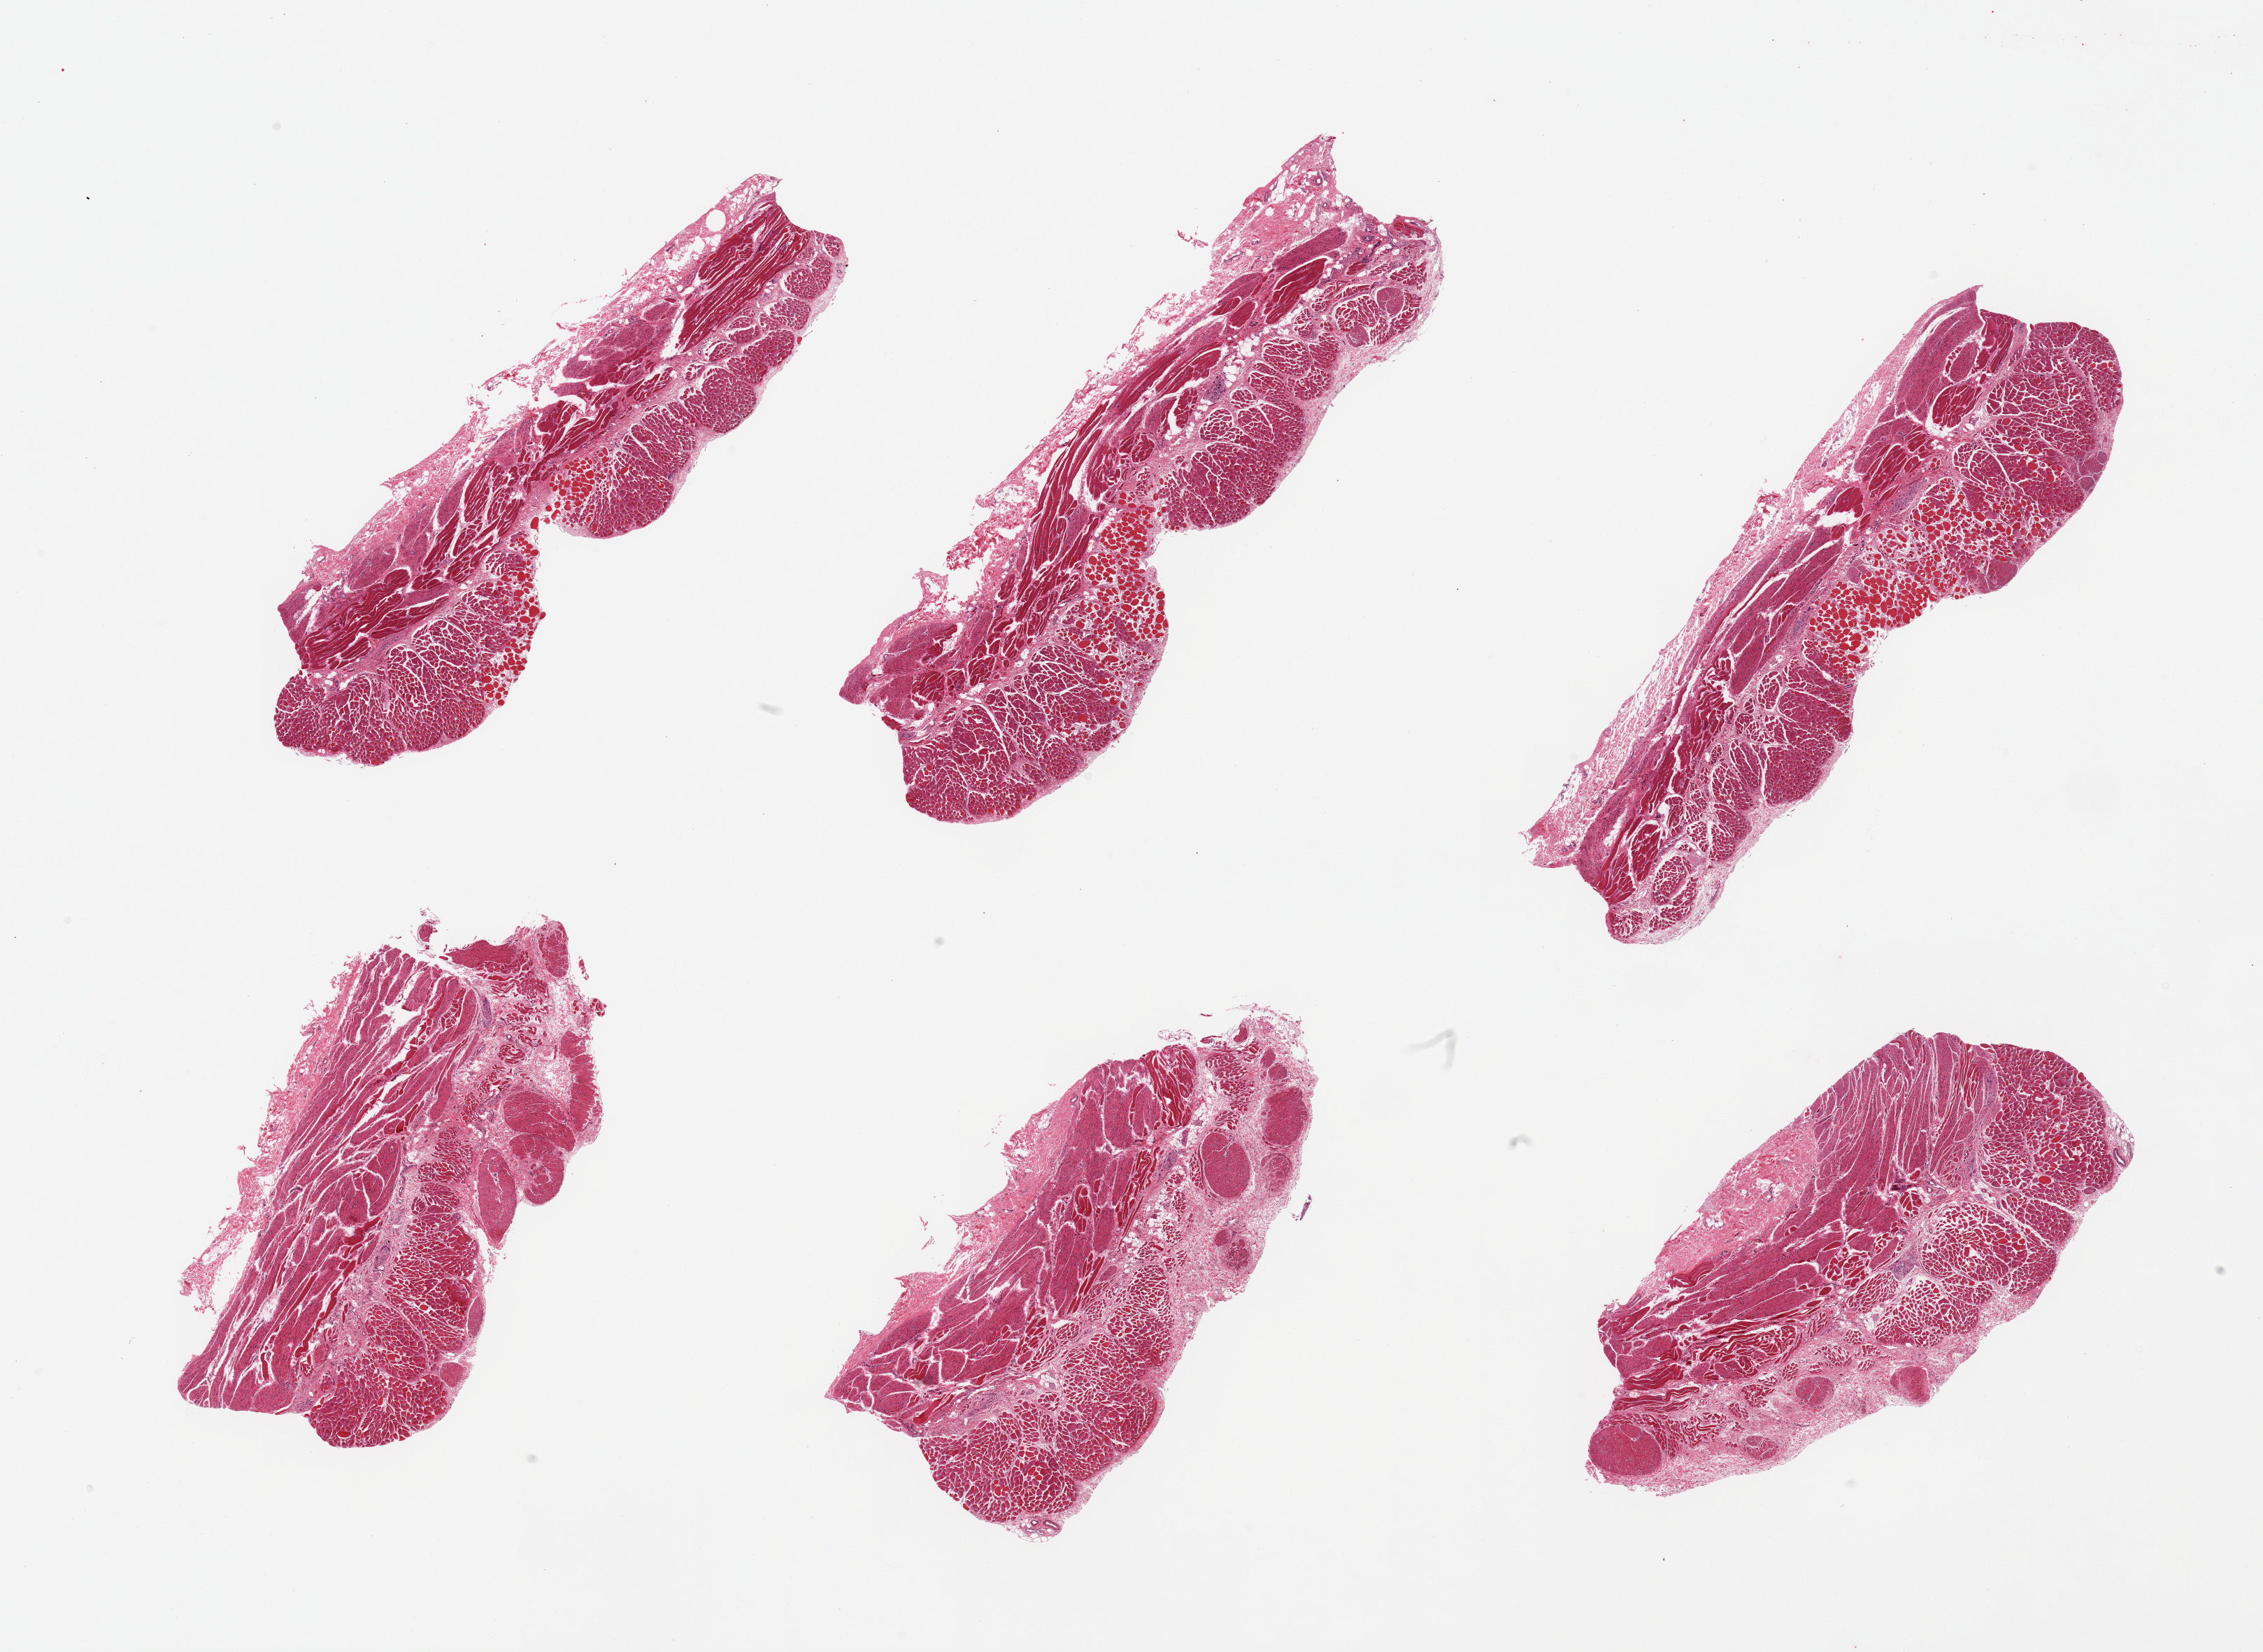
H&E whole-slide image — low-resolution overview of the scanned area, about 25.6 x 18.7 mm, PAXgene-fixed, paraffin-embedded tissue, target tissue: esophageal muscle, tissue donor sample.
Pathologist's review note for this sample: 6 pieces; major admixture of skeletal and smooth muscle indicating sampling of upper esophagus.